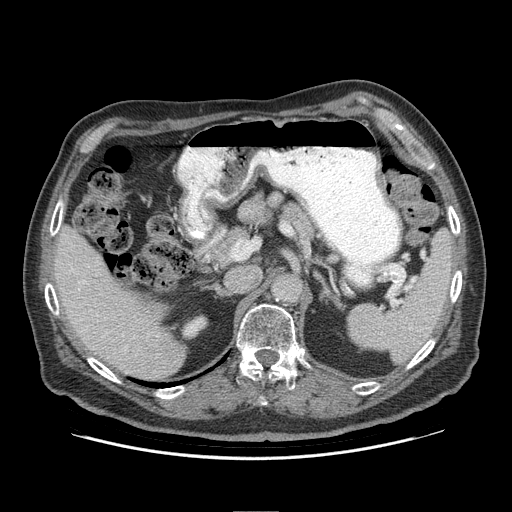
Contrast-enhanced abdominal CT (liver protocol), one axial slice. Slice 54 of 95 in the series (ordered by position). 140 kVp. Soft-tissue window (W 400 / L 40 HU). 2.5 mm slice thickness. 512 × 512 image matrix, field of view 400 × 400 mm. Case-level facts recorded for this patient, not image findings: diagnosis: hepatocellular carcinoma (patient treated with transarterial chemoembolisation; whether this scan precedes or follows treatment is not stated here); TNM stage (as recorded): Stage-IVB; Child-Pugh class: A; tumour nodularity: uninodular.
Annotated regions visible in this slice (semi-automatic segmentation, software-assisted and operator-edited):
- liver parenchyma outside the tumour (the mass and vessels are separate outlines, so this box may not span the whole liver): bounding box <54,226,186,380> (left, top, right, bottom; pixels)